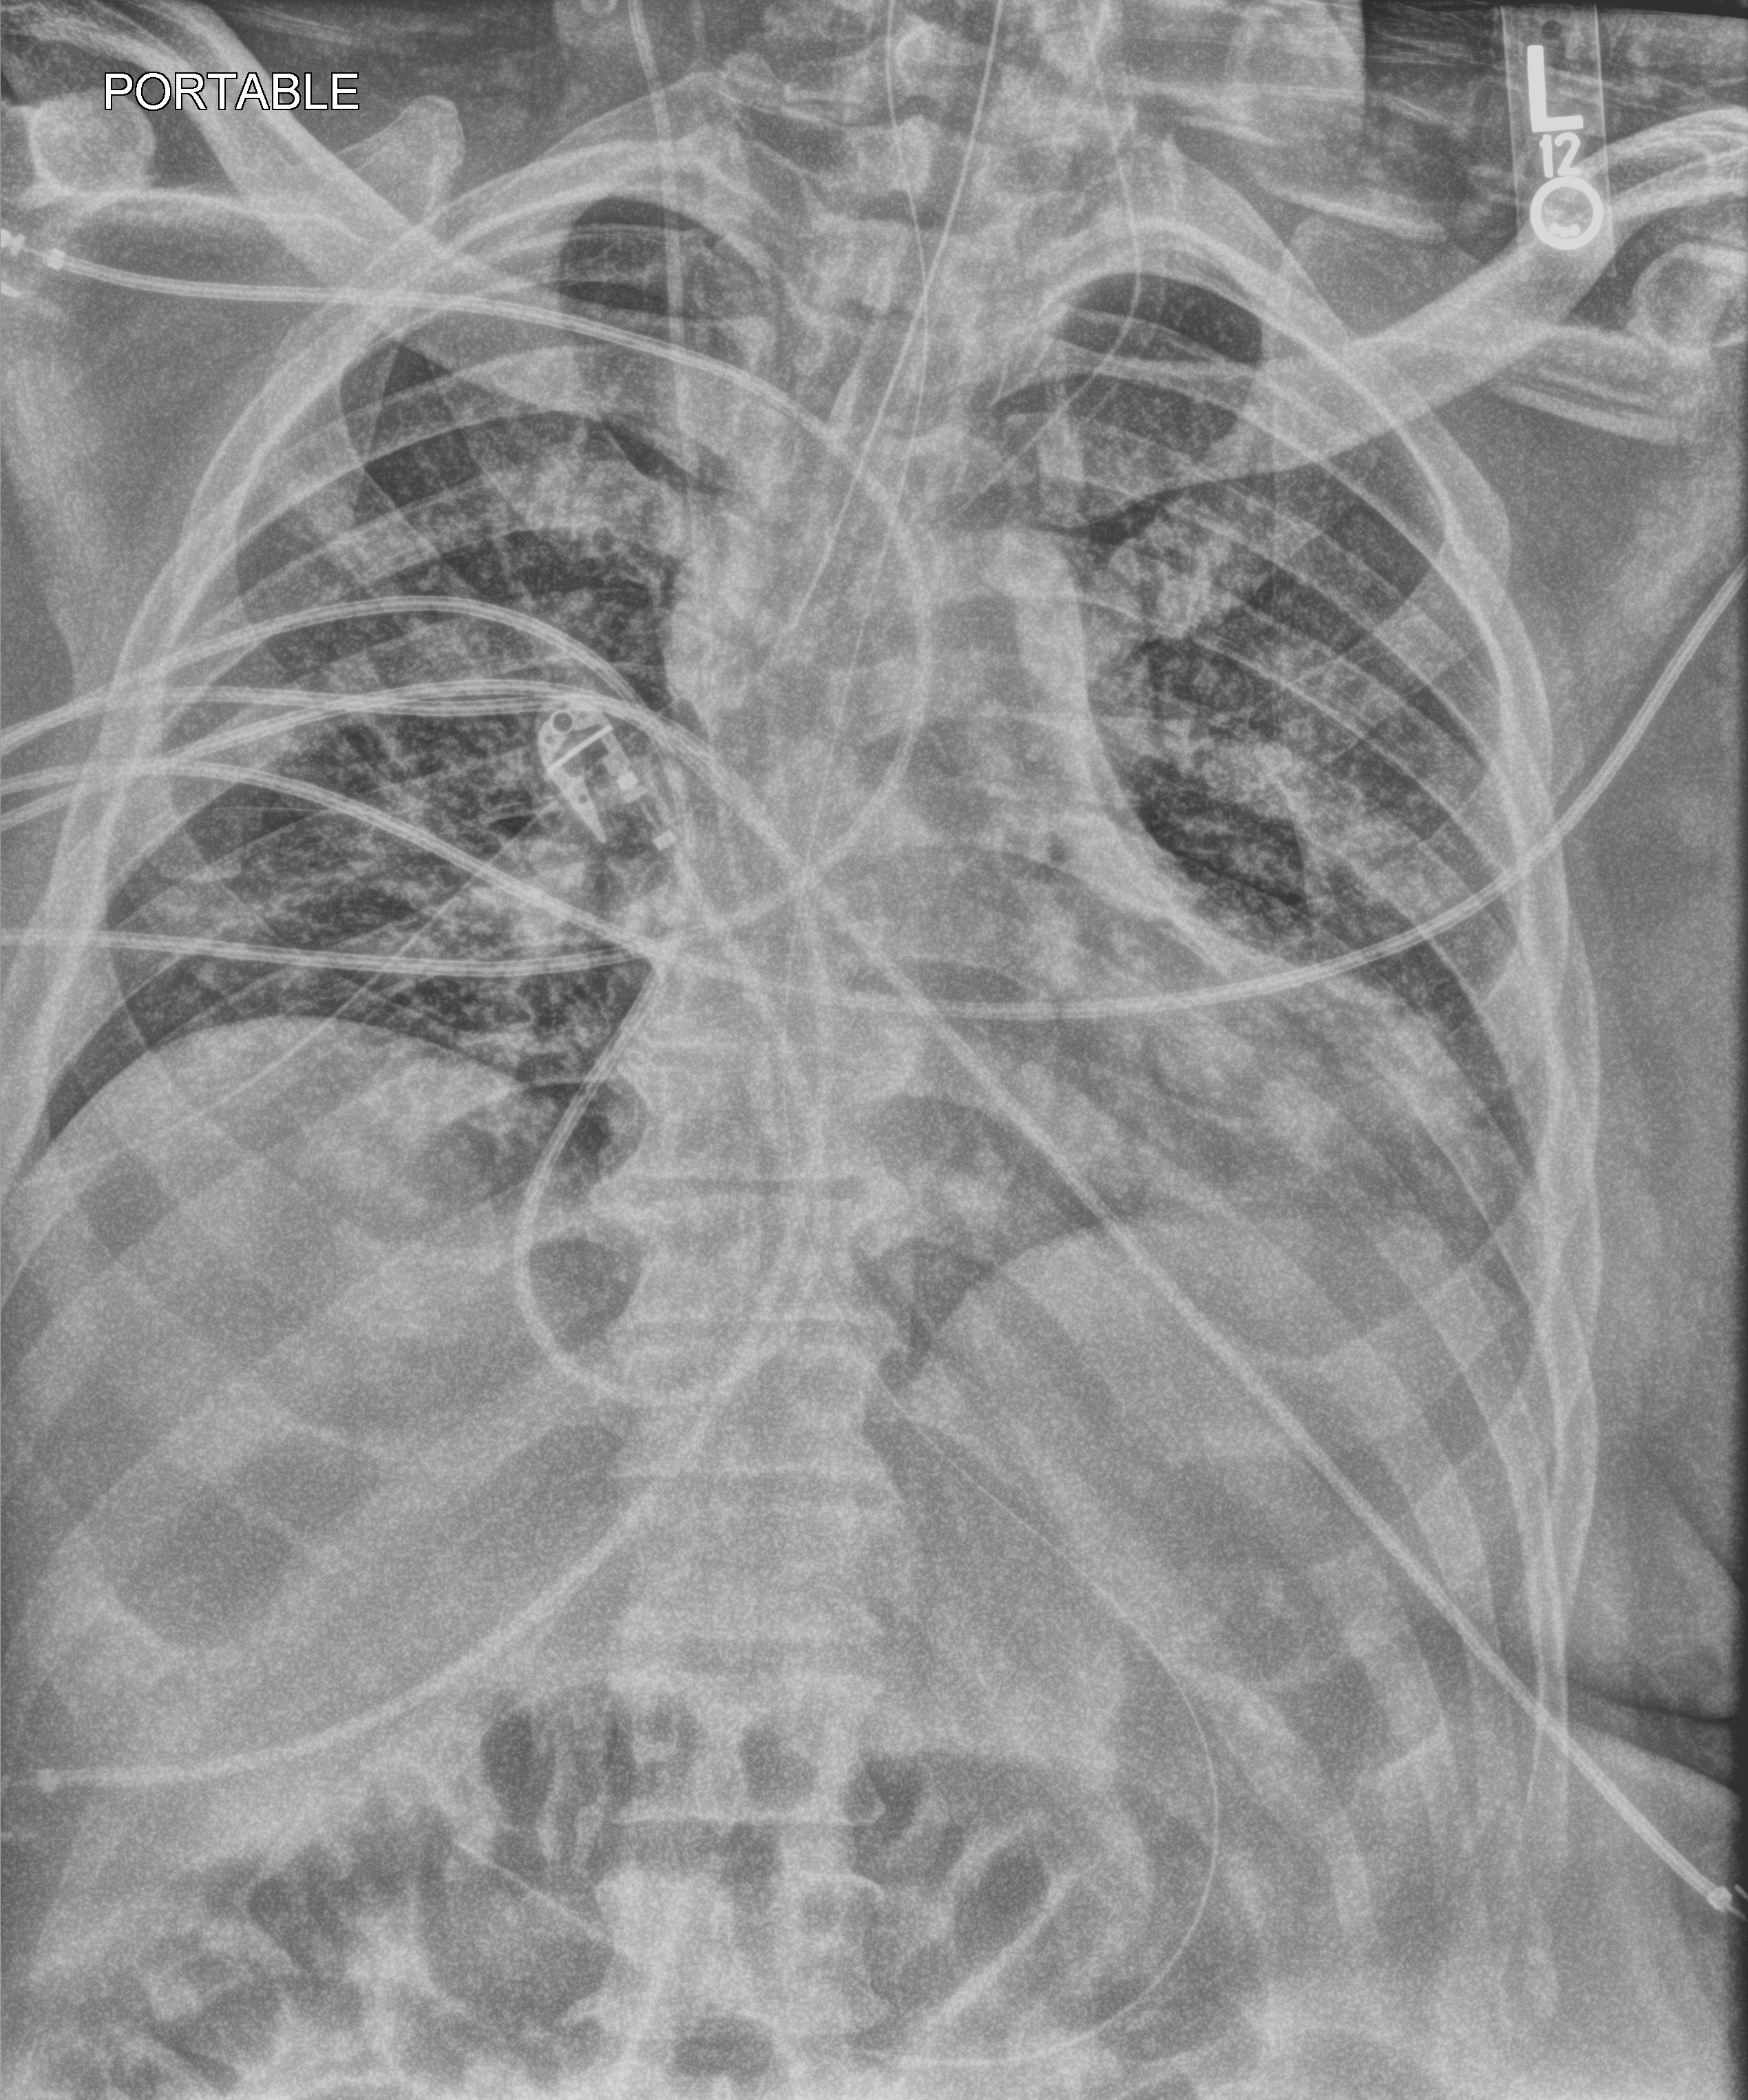
Bedside chest radiograph (computed radiography), anteroposterior (AP) projection. Male patient hospitalised with COVID-19, age 18–59 years.
Admission-level facts for this patient (not findings on this image; timing relative to this image not recorded): diabetes (admission record): no; mechanically ventilated during this hospital stay: yes; admitted to intensive care during this hospital stay: yes.